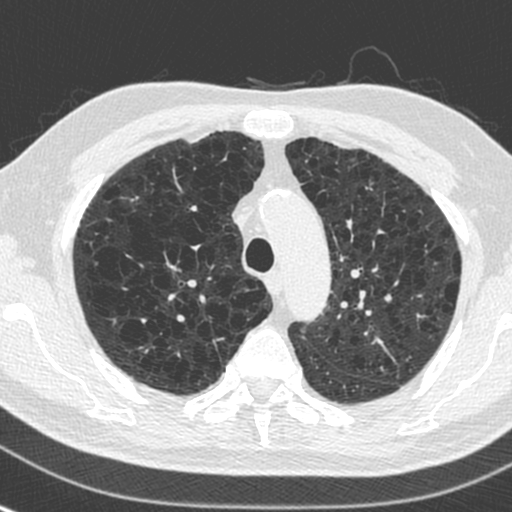
Axial slice from a low-dose chest CT screening exam. Baseline screening round. Lung window (W 1500 / L -600 HU). Standard (soft-tissue) reconstruction kernel (C). 120 kVp. 512 × 512 image matrix, field of view 305 × 305 mm. Male participant, aged 73 years at enrolment. Current smoker at enrolment.
• Expert reader's lesion annotation, bounding box <154,250,200,287> (left, top, right, bottom; pixels).
• Screening reader's record for this exam: no non-calcified nodule ≥4 mm recorded.
• Later outcome: lung cancer diagnosed 446 days after this screen (after the second annual screen) — squamous cell carcinoma, NOS, right upper lobe, stage IA (AJCC 6th edition), 10 mm at pathology.